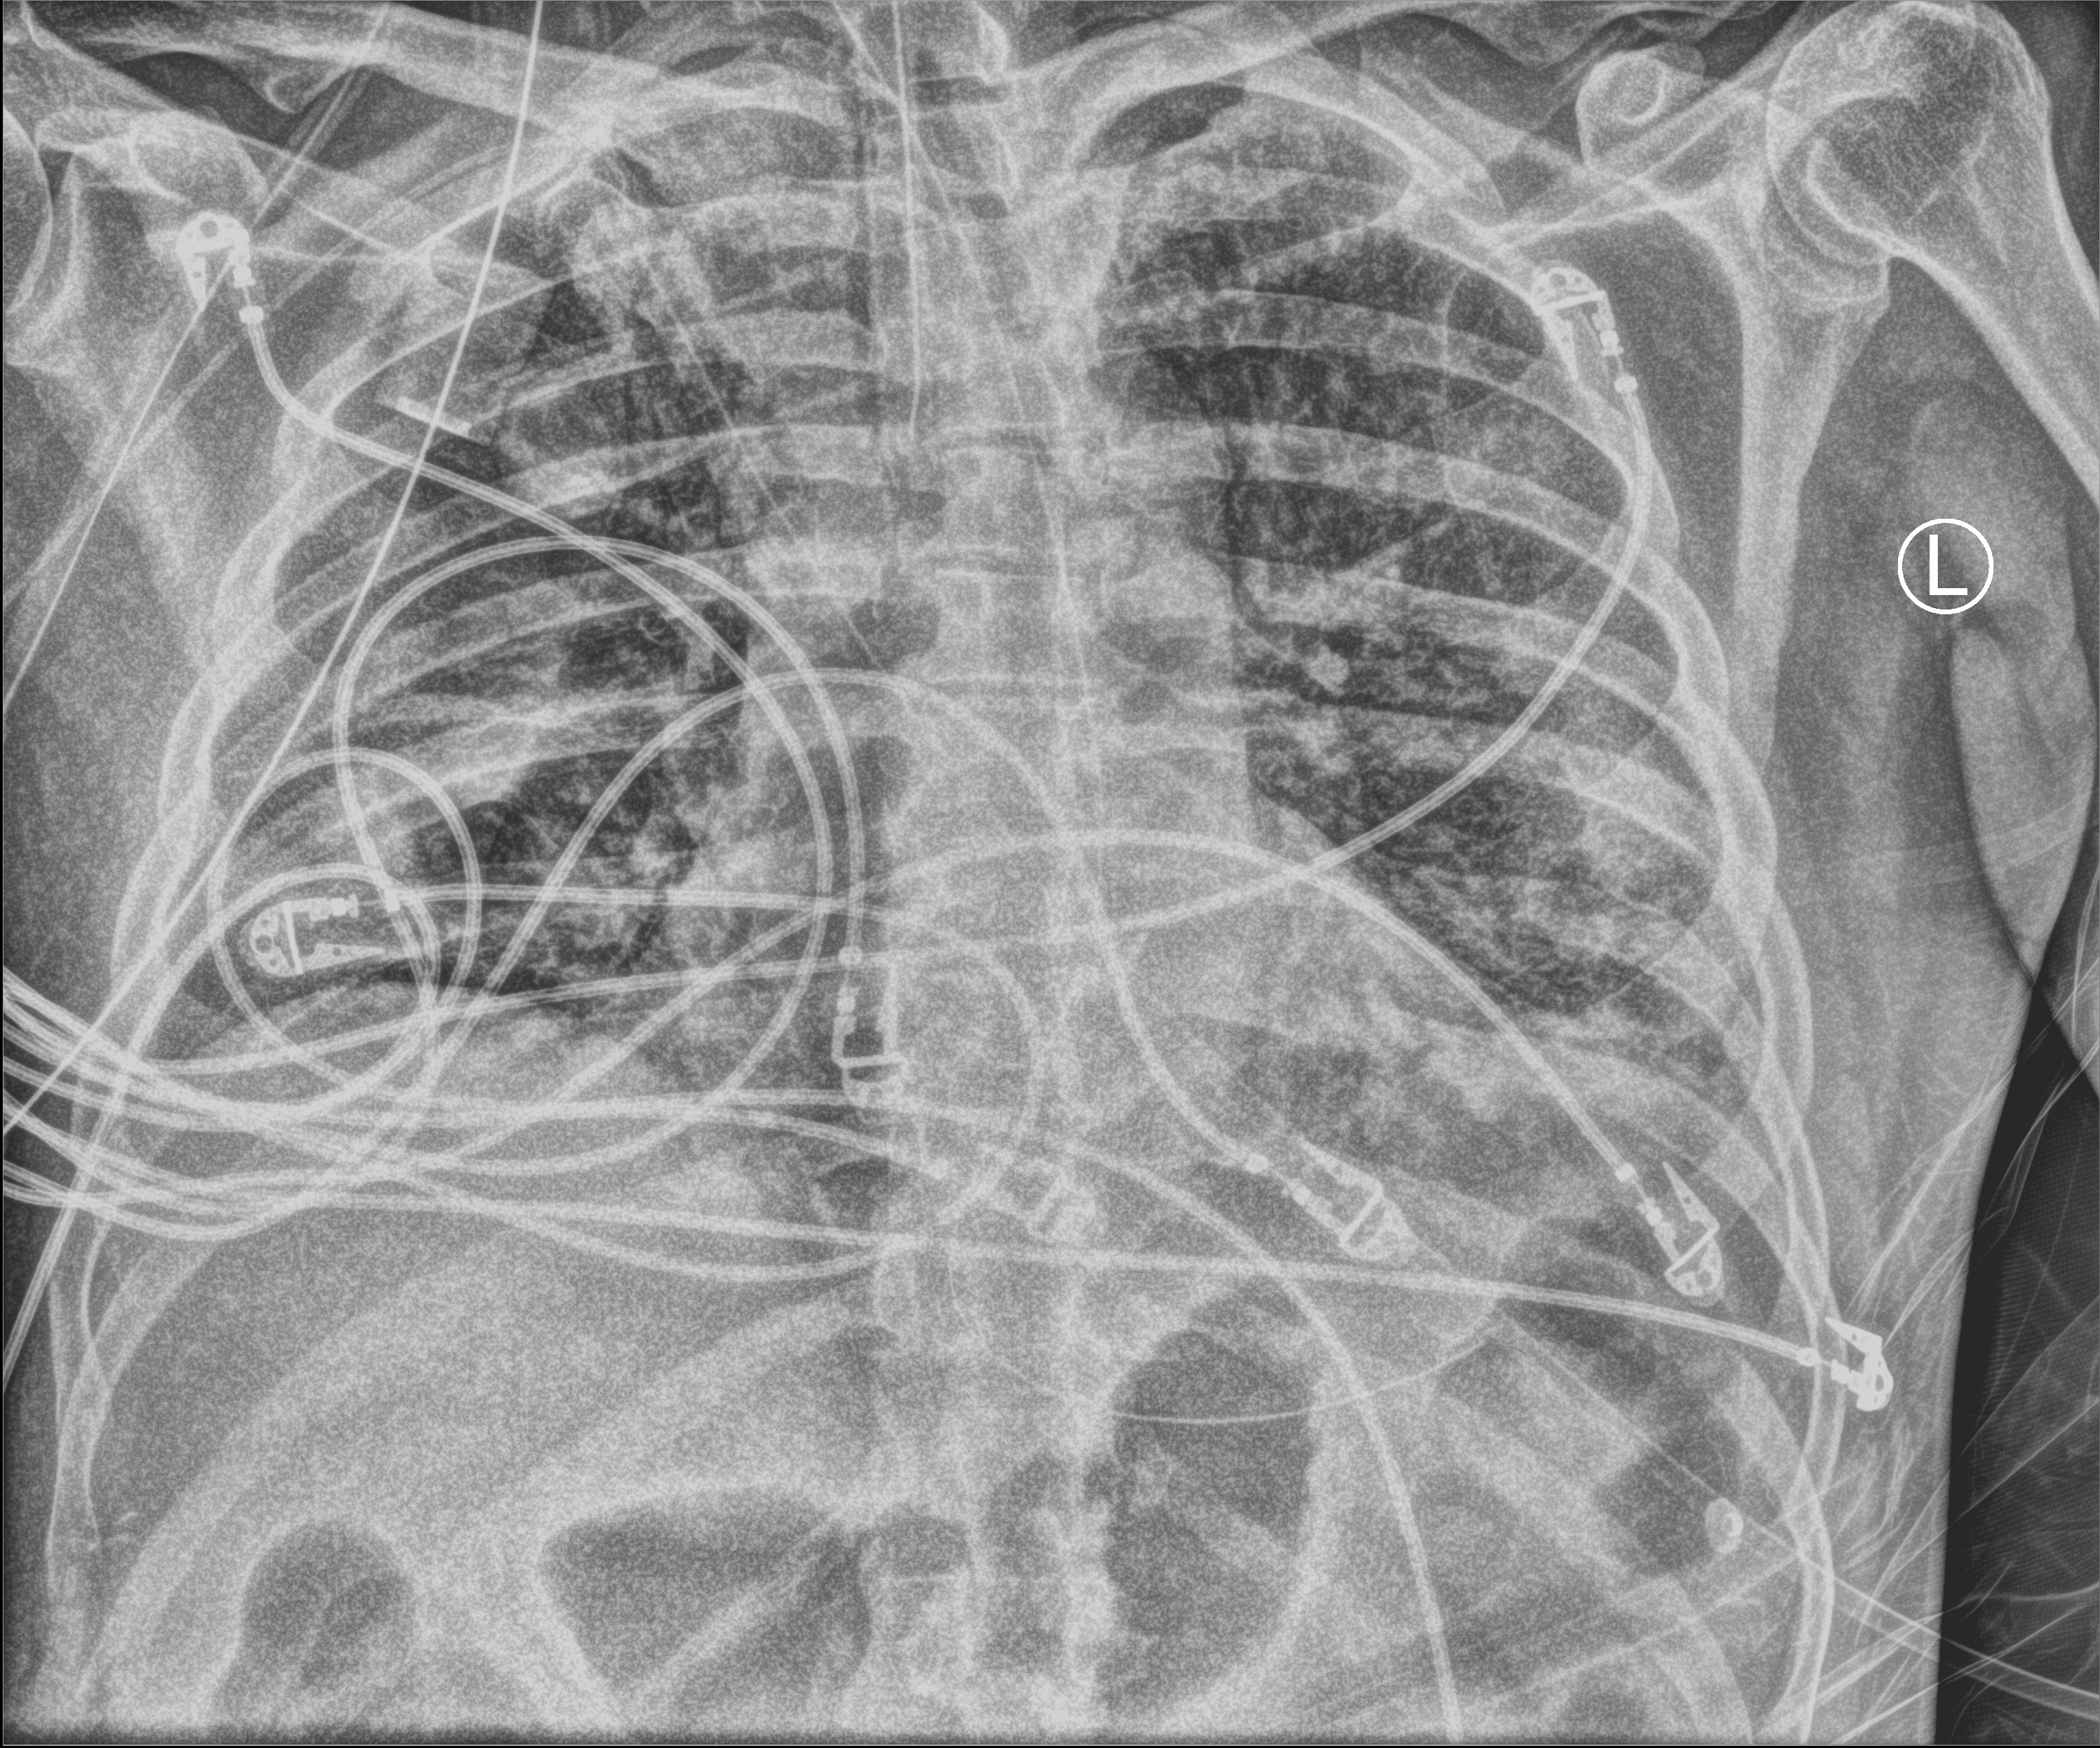
Bedside chest radiograph (computed radiography); anteroposterior (AP) projection. Patient hospitalised with COVID-19; male, aged 60–74 years.
Admission-level facts for this patient (not findings on this image; timing relative to this image not recorded):
- admitted to intensive care during this hospital stay: yes